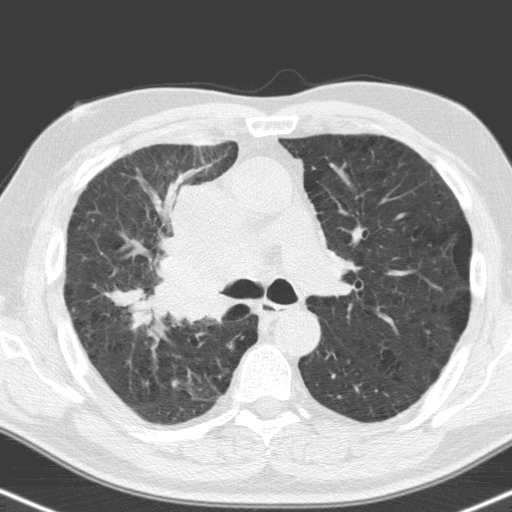
Low-dose screening chest CT, one axial slice; position 106 of 160 along the scan axis; 120 kVp; lung window (W 1500 / L -600 HU); 3.2 mm slice thickness; 512 × 512 image matrix, field of view 324 × 324 mm.
Outlined on this slice (expert manual segmentation):
- lesion 1 (tumor, hilum of right lung): bounding box (x1, y1, x2, y2) in pixels: (154, 185, 263, 317)
- lesion 2 (tumor, upper lobe of right lung): (113, 289, 135, 306)